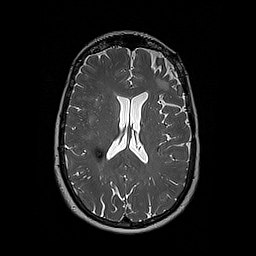
Brain MRI from a brain-tumour surgery series, one axial slice. Slice 109 of 192 in the series (ordered by position). 1 mm slice thickness. 256 × 256 image matrix, field of view 250 × 250 mm. Case-level facts recorded for this patient, not image findings: histopathology: Oligodendroglioma; WHO grade: 2; IDH mutation: yes.
Structures marked on this image (manually delineated by an expert):
- tumour: box from (x=156, y=79) to (x=161, y=87) px